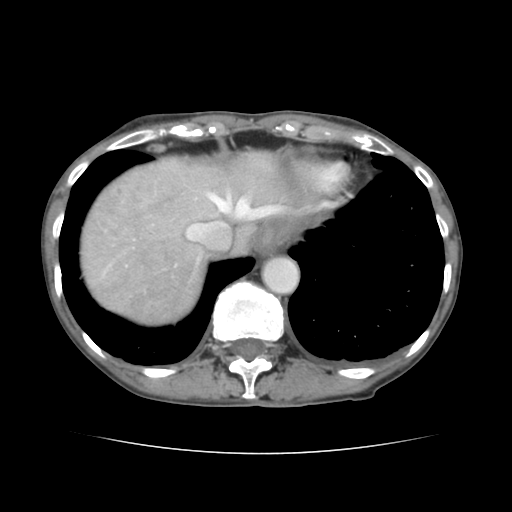
Contrast-enhanced abdominal CT, one axial slice; position 122 of 136 along the scan axis; 120 kVp; intravenous contrast given; soft-tissue window (W 400 / L 40 HU); 2.5 mm slice thickness; 512 × 512 image matrix. Female patient, age 77 years. From the clinical record (not read from this slice): diagnosis: colorectal cancer liver metastases, imaged before liver resection; multiple liver metastases: yes; largest metastasis: 3 cm; disease in both lobes: no.
Outlined on this slice (manually delineated by an expert):
- hepatic veins: bounding box [x1, y1, x2, y2] px = [111, 190, 278, 264]
- liver: [81, 153, 293, 323]
- planned liver remnant (the part of the liver to remain after resection): [181, 153, 296, 249]